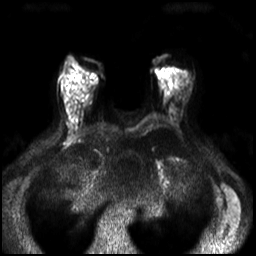
Breast MRI, one axial slice; slice 15 of 30 in the series (ordered by position); diffusion-weighted series; image 2 of 4 stored at this slice position (different b-values; order by instance number); 3 T; 256 × 256 image matrix. Female patient.
Outlined on this slice (expert manual segmentation):
- tumour on diffusion-weighted imaging: bounding box <78,87,91,98> (left, top, right, bottom; pixels)